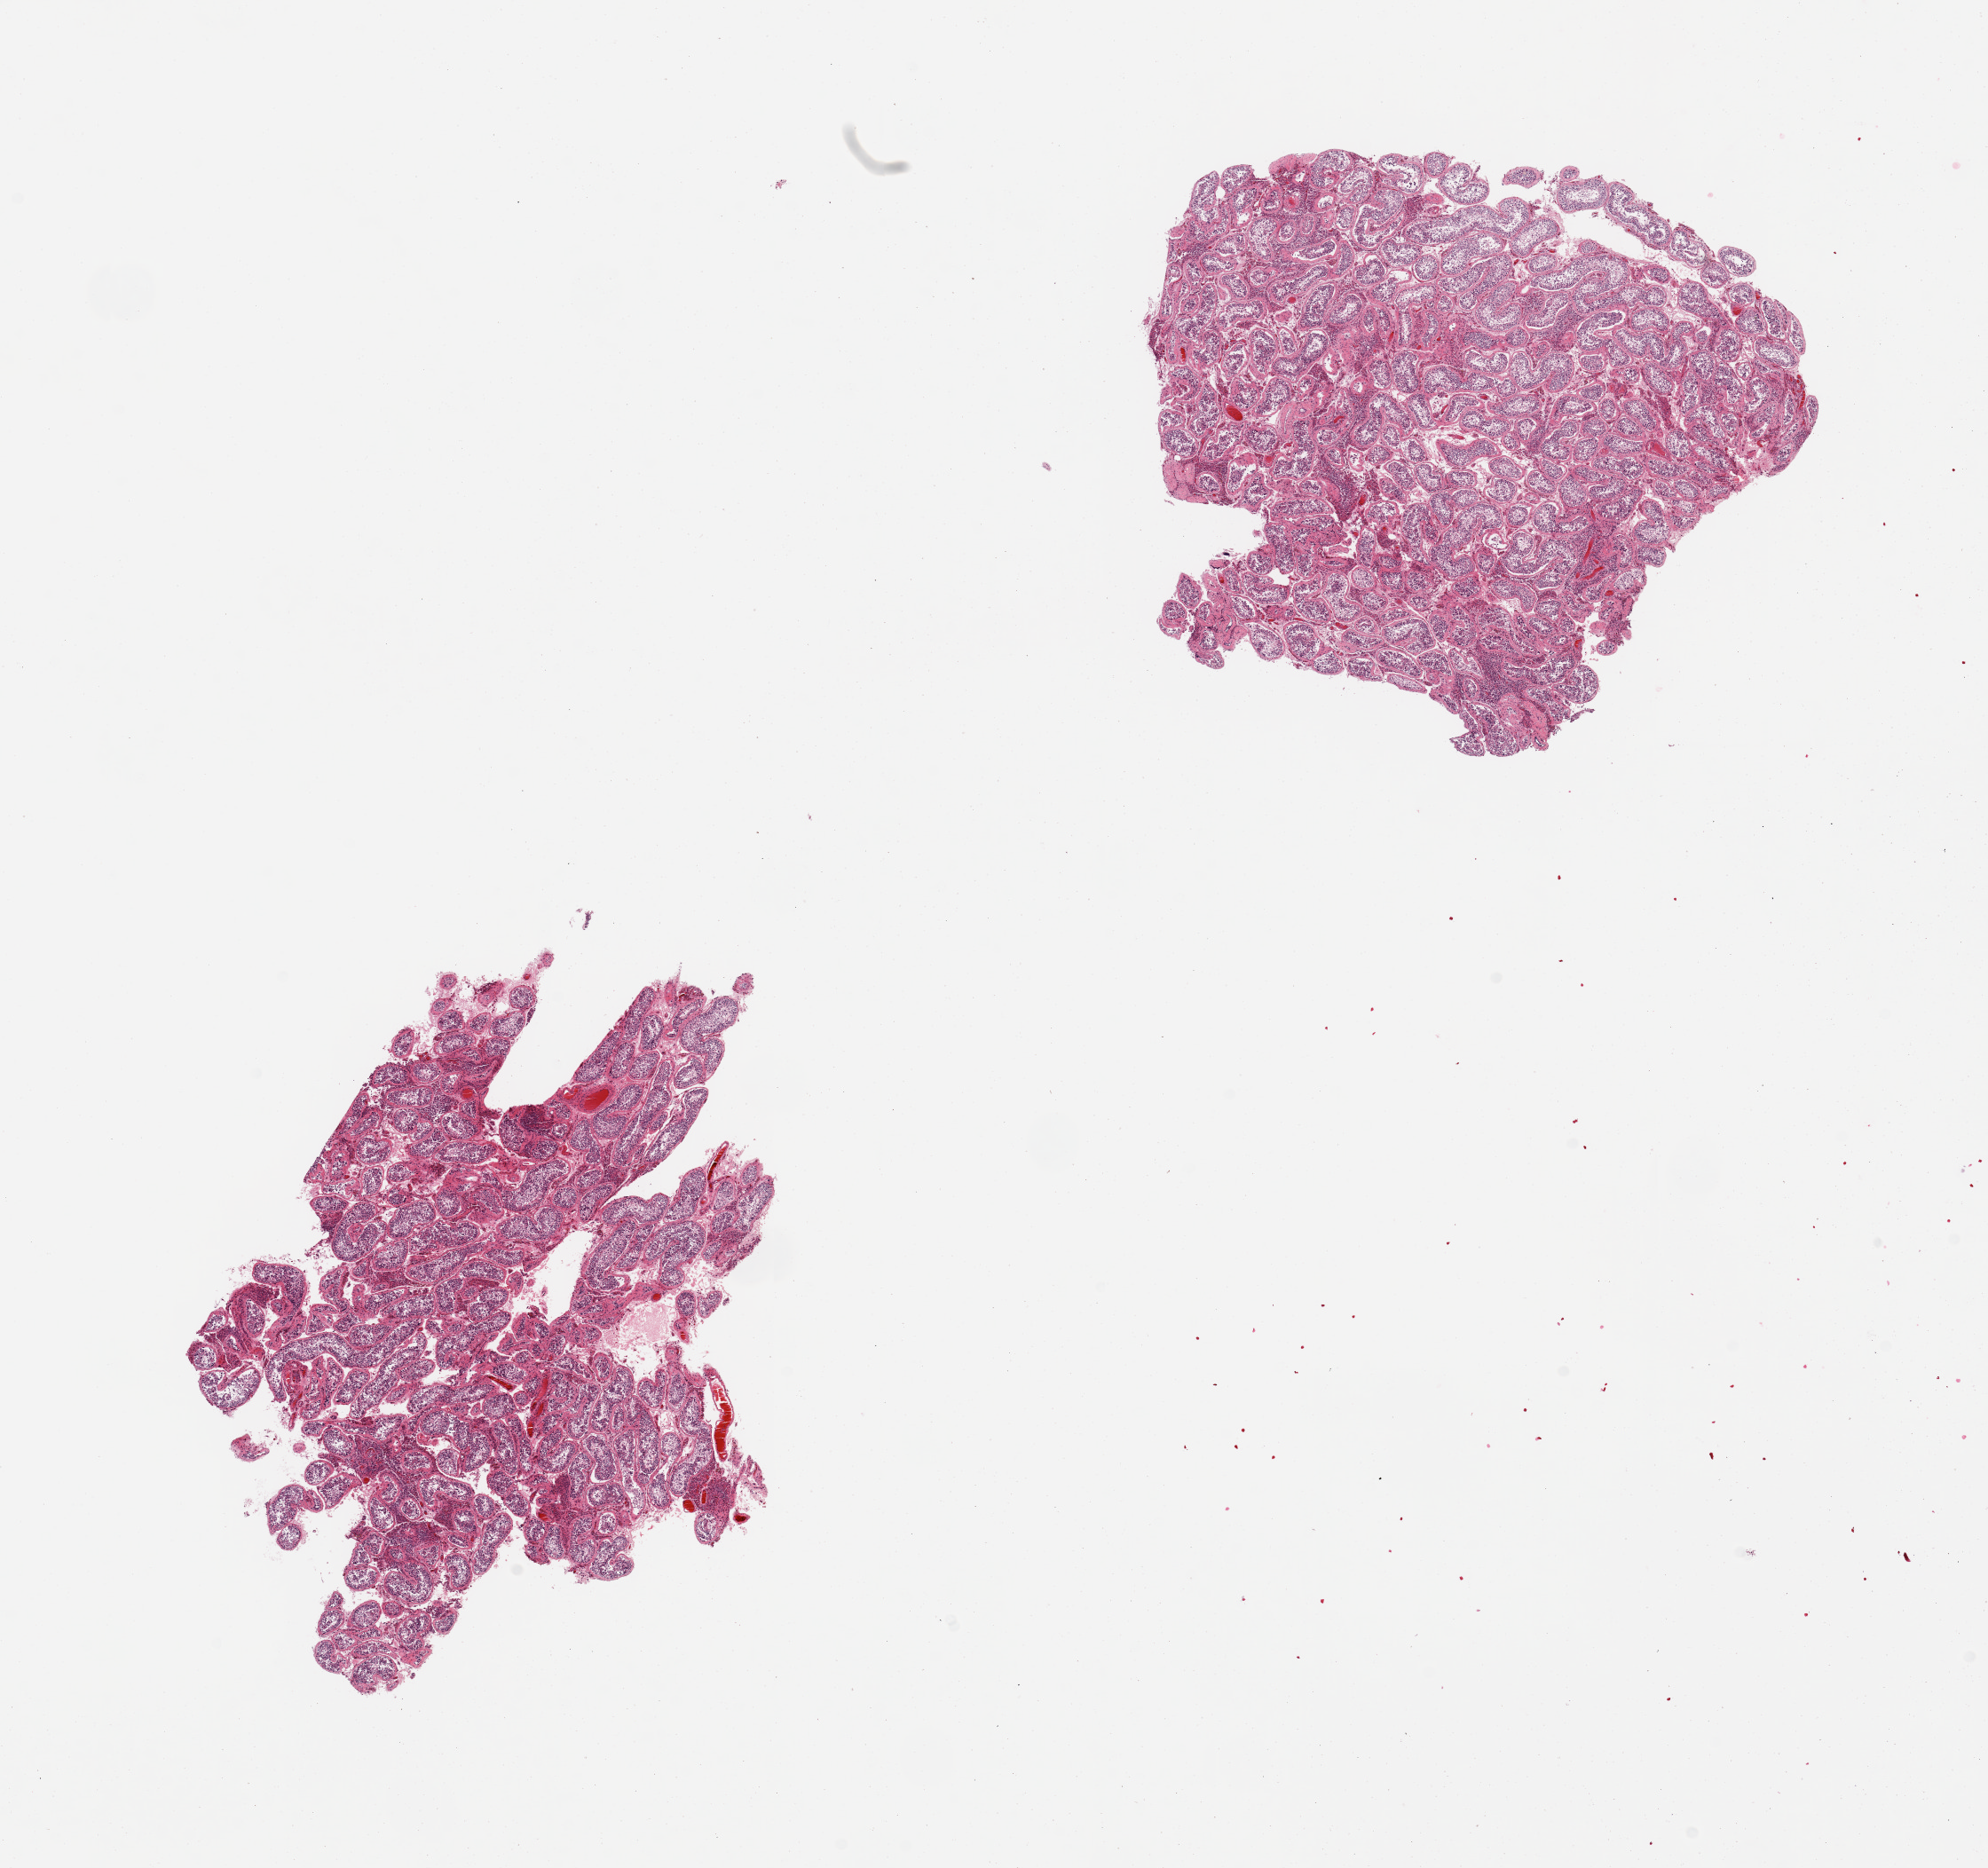
Whole-slide image, H&E stain — shown as a low-resolution overview of the whole scanned area (about 17.7 x 16.7 mm); PAXgene-fixed paraffin-embedded (PFPE) section; section of testis (target tissue); donor tissue sample. Donor sex: male.
- review note (as recorded): 2 pieces, spermatogenesis present